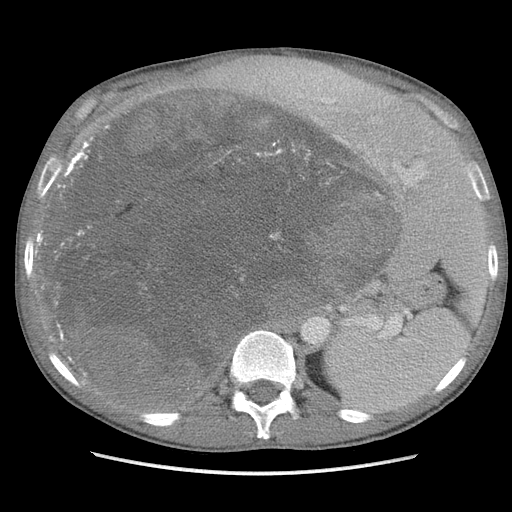
Contrast-enhanced abdominal CT, one axial slice; position 73 of 115 along the scan axis; soft-tissue window (W 400 / L 40 HU); 5 mm slice thickness; 512 × 512 image matrix. Male patient. From the clinical record (not read from this slice): diagnosis: adrenocortical carcinoma; tumour side: right adrenal; Ki-67 index: 13 %.
Outlined on this slice (semi-automatically segmented with operator editing):
- mass: bounding box [x1, y1, x2, y2] px = [56, 87, 390, 407]